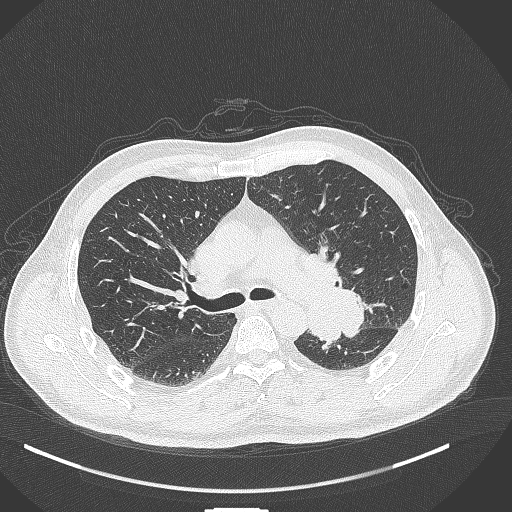
Chest CT, one axial slice. Slice 266 of 429 in the series (ordered by position). Lung window (W 1500 / L -600 HU). 512 × 512 image matrix. Male patient, age 55 years. From the clinical record (not read from this slice): clinical TNM (as recorded): T3 N0 M1c.
Annotated regions visible in this slice (bounding box drawn by a radiologist):
- lung tumour (recorded histology: adenocarcinoma): bounding box <300,272,371,350> (left, top, right, bottom; pixels)